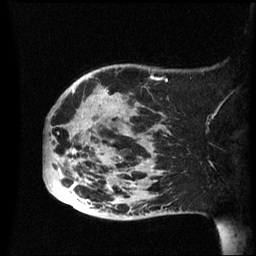
Breast MRI (dynamic contrast-enhanced), one sagittal slice. Slice 16 of 60 in the series (ordered by position). Dynamic contrast-enhanced series, image 2 of 3 at this slice position (ordered by acquisition). 1.5 T. TE 4.2 ms, TR 8.4 ms. 2.4 mm slice thickness. 256 × 256 image matrix. Female patient, age 49 years.
Outlined on this slice (semi-automatically segmented with operator editing):
- analysis volume of interest (the breast-tissue region the enhancement analysis was run in; not a lesion): bounding box <43,64,174,220> (left, top, right, bottom; pixels)
- tumour enhancement mask (voxels above the 70 % enhancement threshold inside the analysis volume of interest): <73,90,153,217>